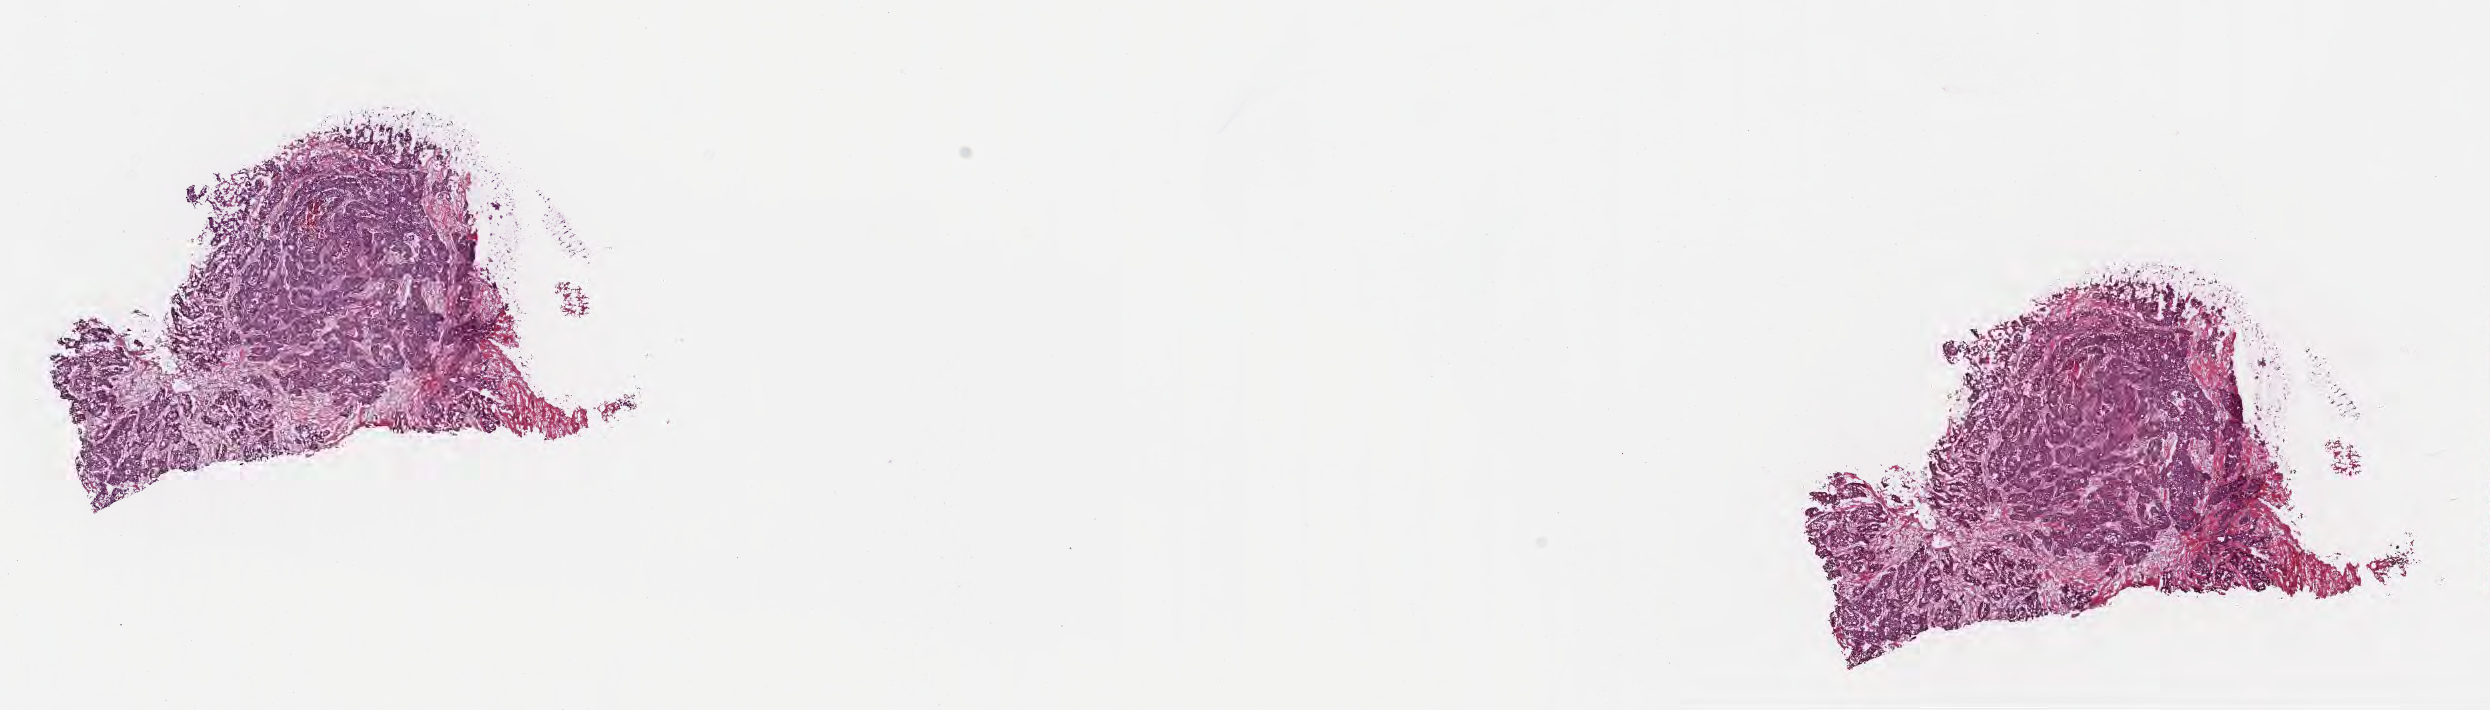
Whole-slide image, haematoxylin and eosin stain — low-resolution overview of the scanned area, about 20.1 x 5.7 mm. Cryosection. Metastatic tumor tissue, resected from lymph node. Female patient; age at initial diagnosis 76 years. Slide review estimates, as recorded: tumor cells 75%, tumor nuclei 80%, stromal cells 25%, necrosis 0%, normal cells 0%. Inflammatory infiltration, as recorded: lymphocyte infiltration 0%, monocyte infiltration 0%, neutrophil infiltration 0%.
Patient diagnosis (primary): Adenocarcinoma, metastatic, NOS. Section: top of the tissue portion.